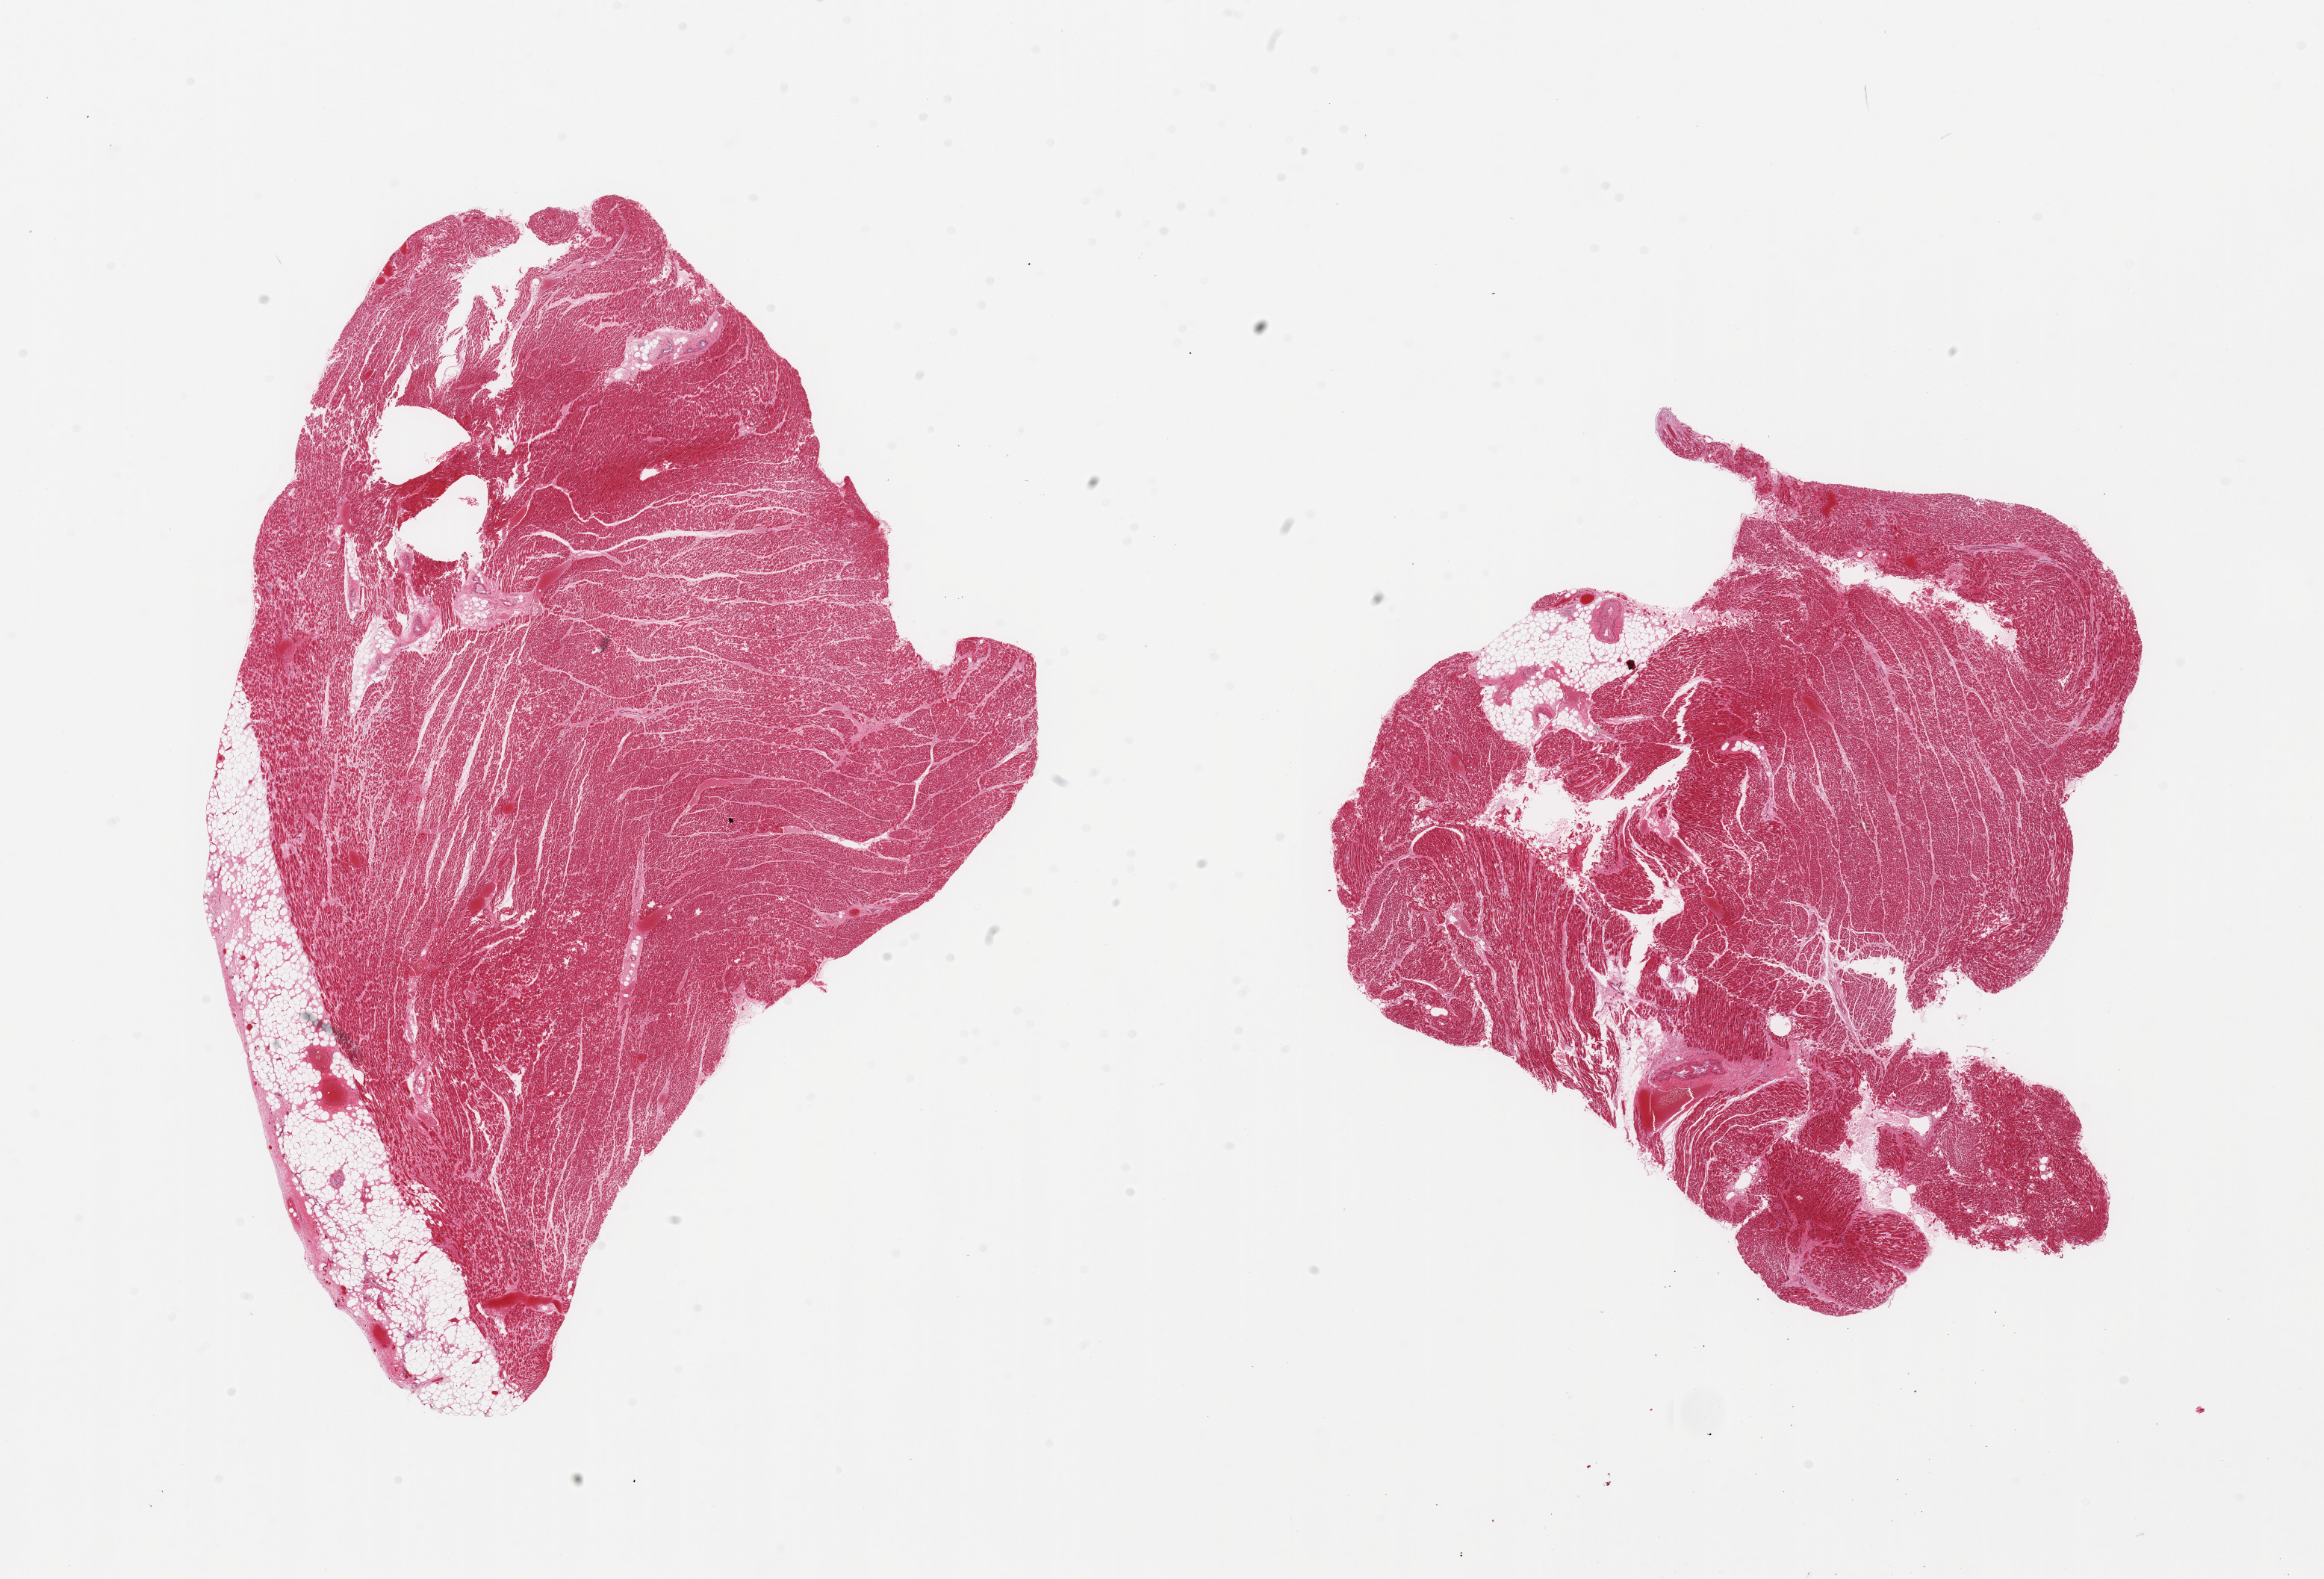
Whole-slide image, H&E stain, brightfield, shown as a low-resolution overview of the whole scanned area (about 24.6 x 16.7 mm). PAXgene-fixed, paraffin-embedded tissue. Target tissue: heart. Tissue donor sample. Female donor.
Review note (as recorded): 2 pieces, interstitial fibrosis/chronic ischemic change, epicardial fat up to ~1mm.